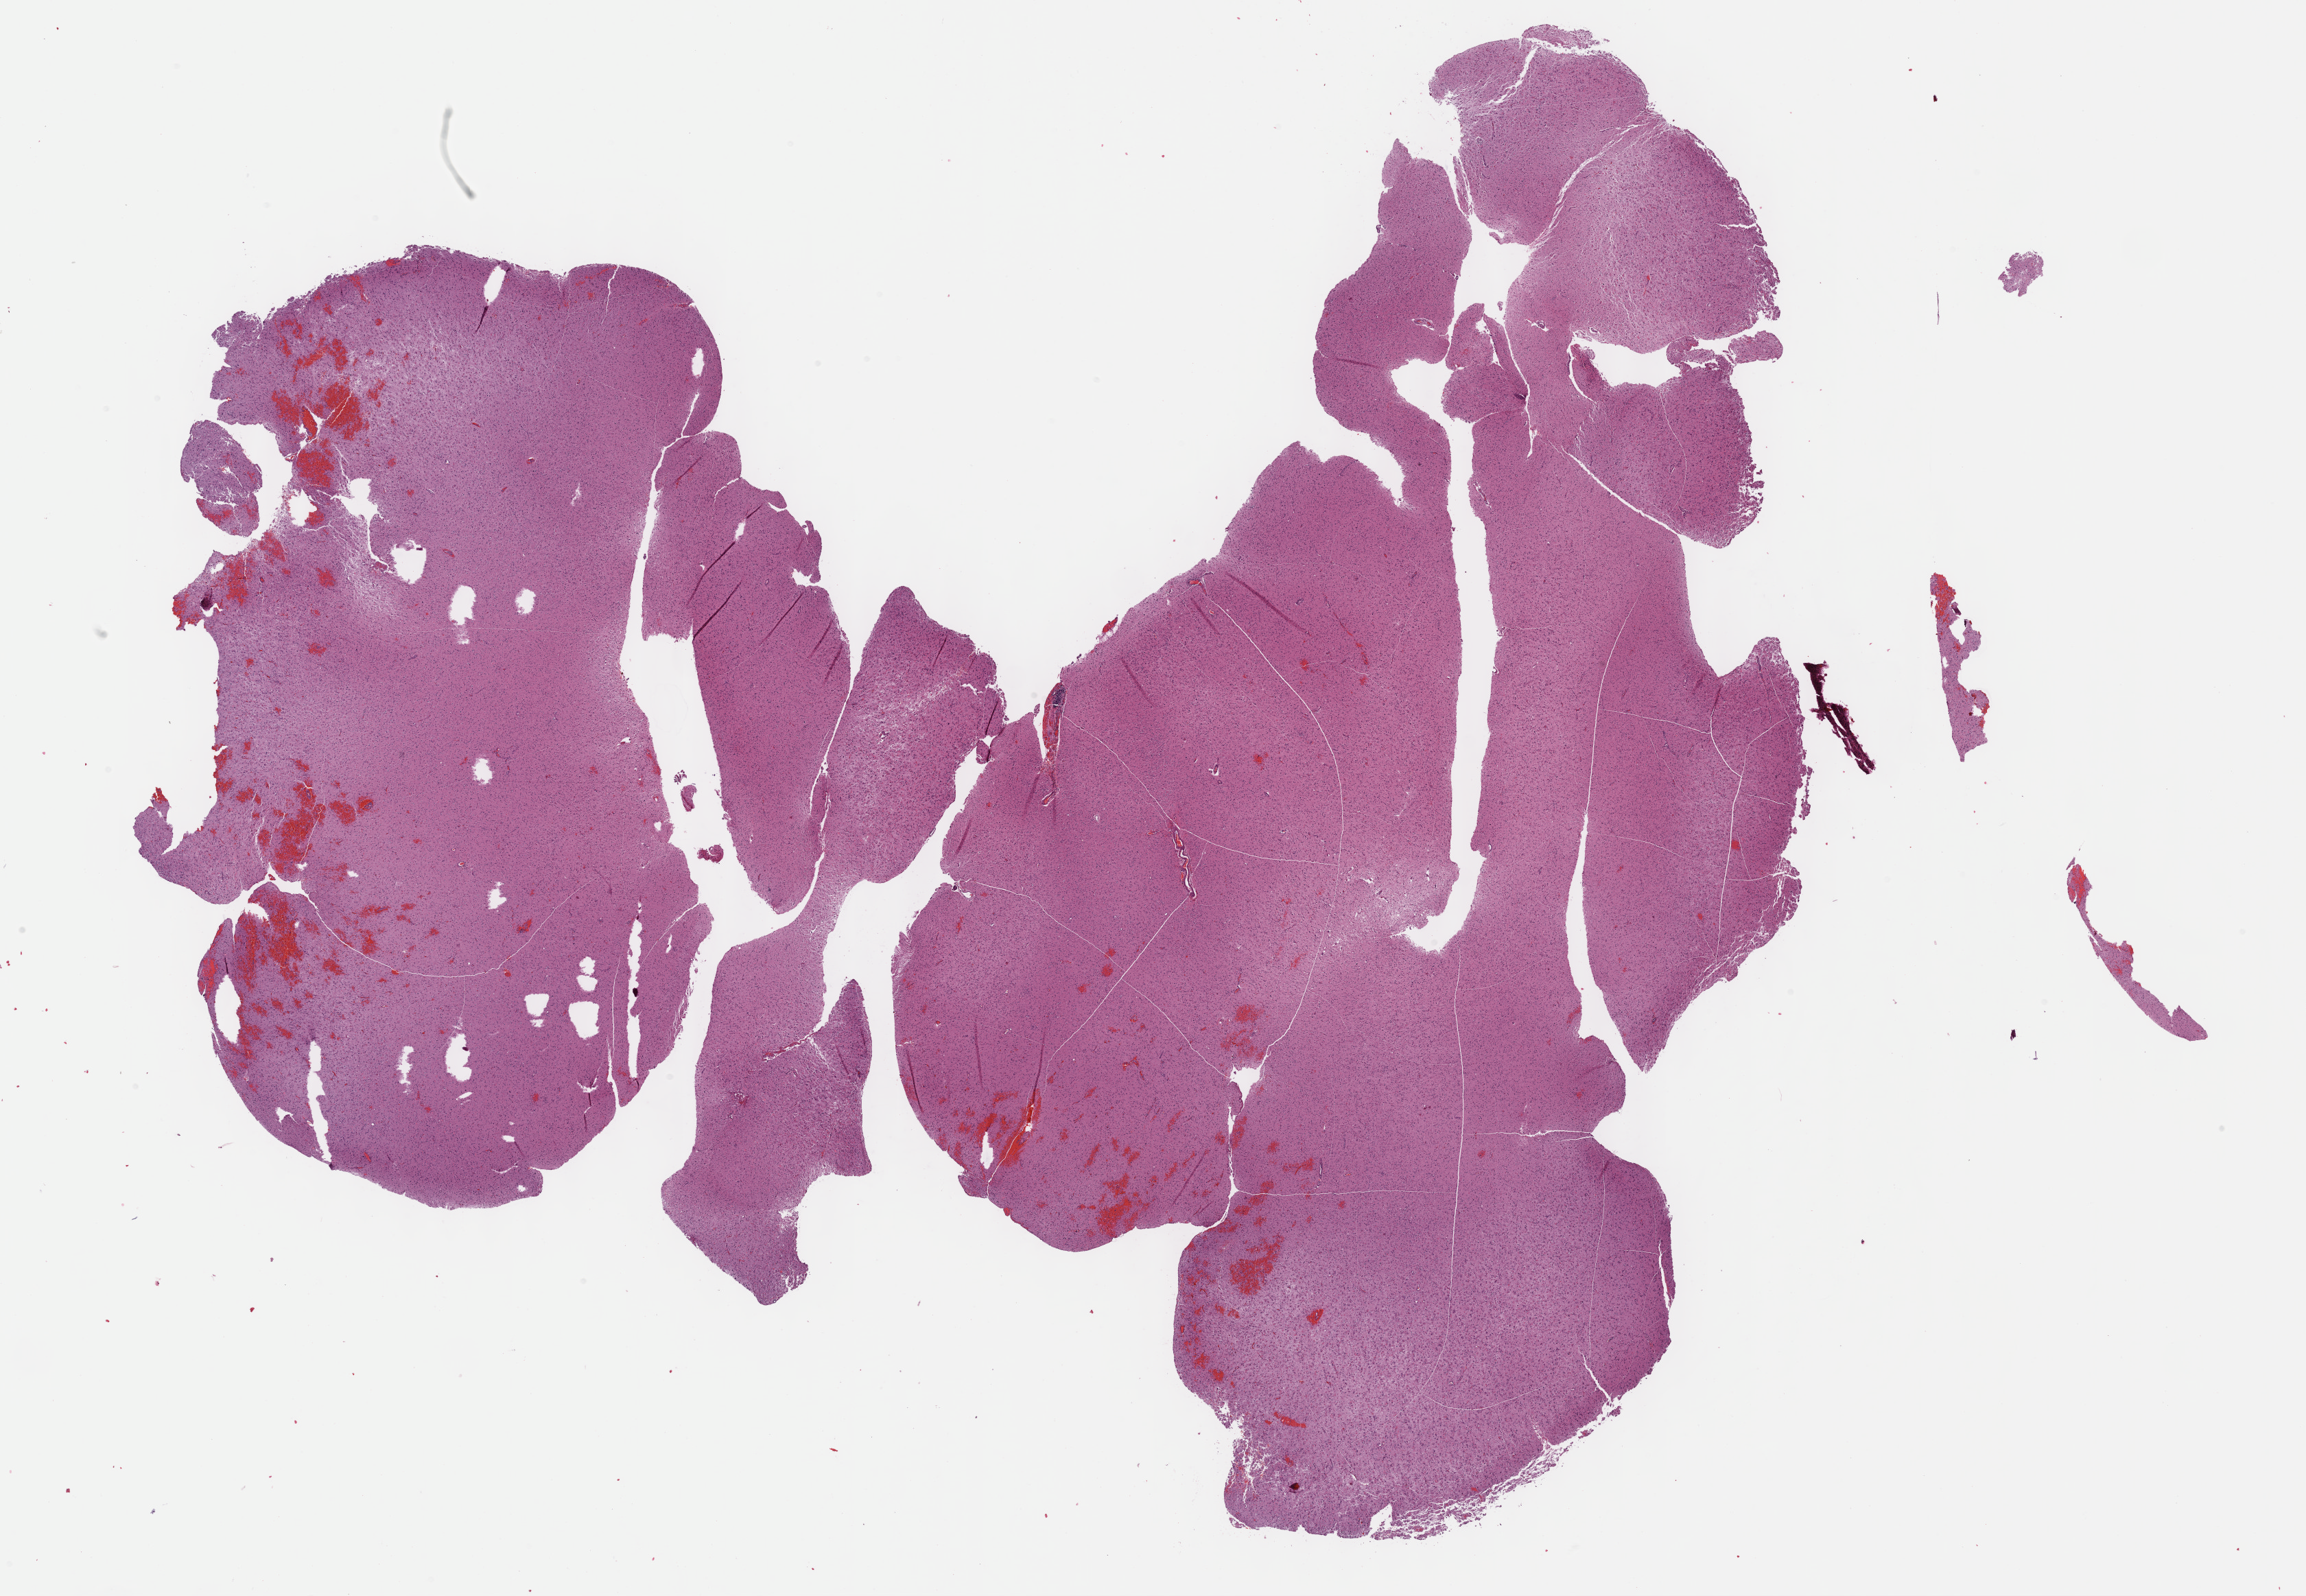
Digitized H&E-stained tissue section (whole slide), low-resolution overview of the scanned area, about 27.2 x 18.8 mm (acquisition: 40x scan). Formalin-fixed paraffin-embedded (FFPE) diagnostic section. Primary tumour sample from the brain. Patient: female, age at initial diagnosis 30 years. Histologic grade: G3 (poorly differentiated).
Diagnosis: Astrocytoma, anaplastic. Laterality: left.